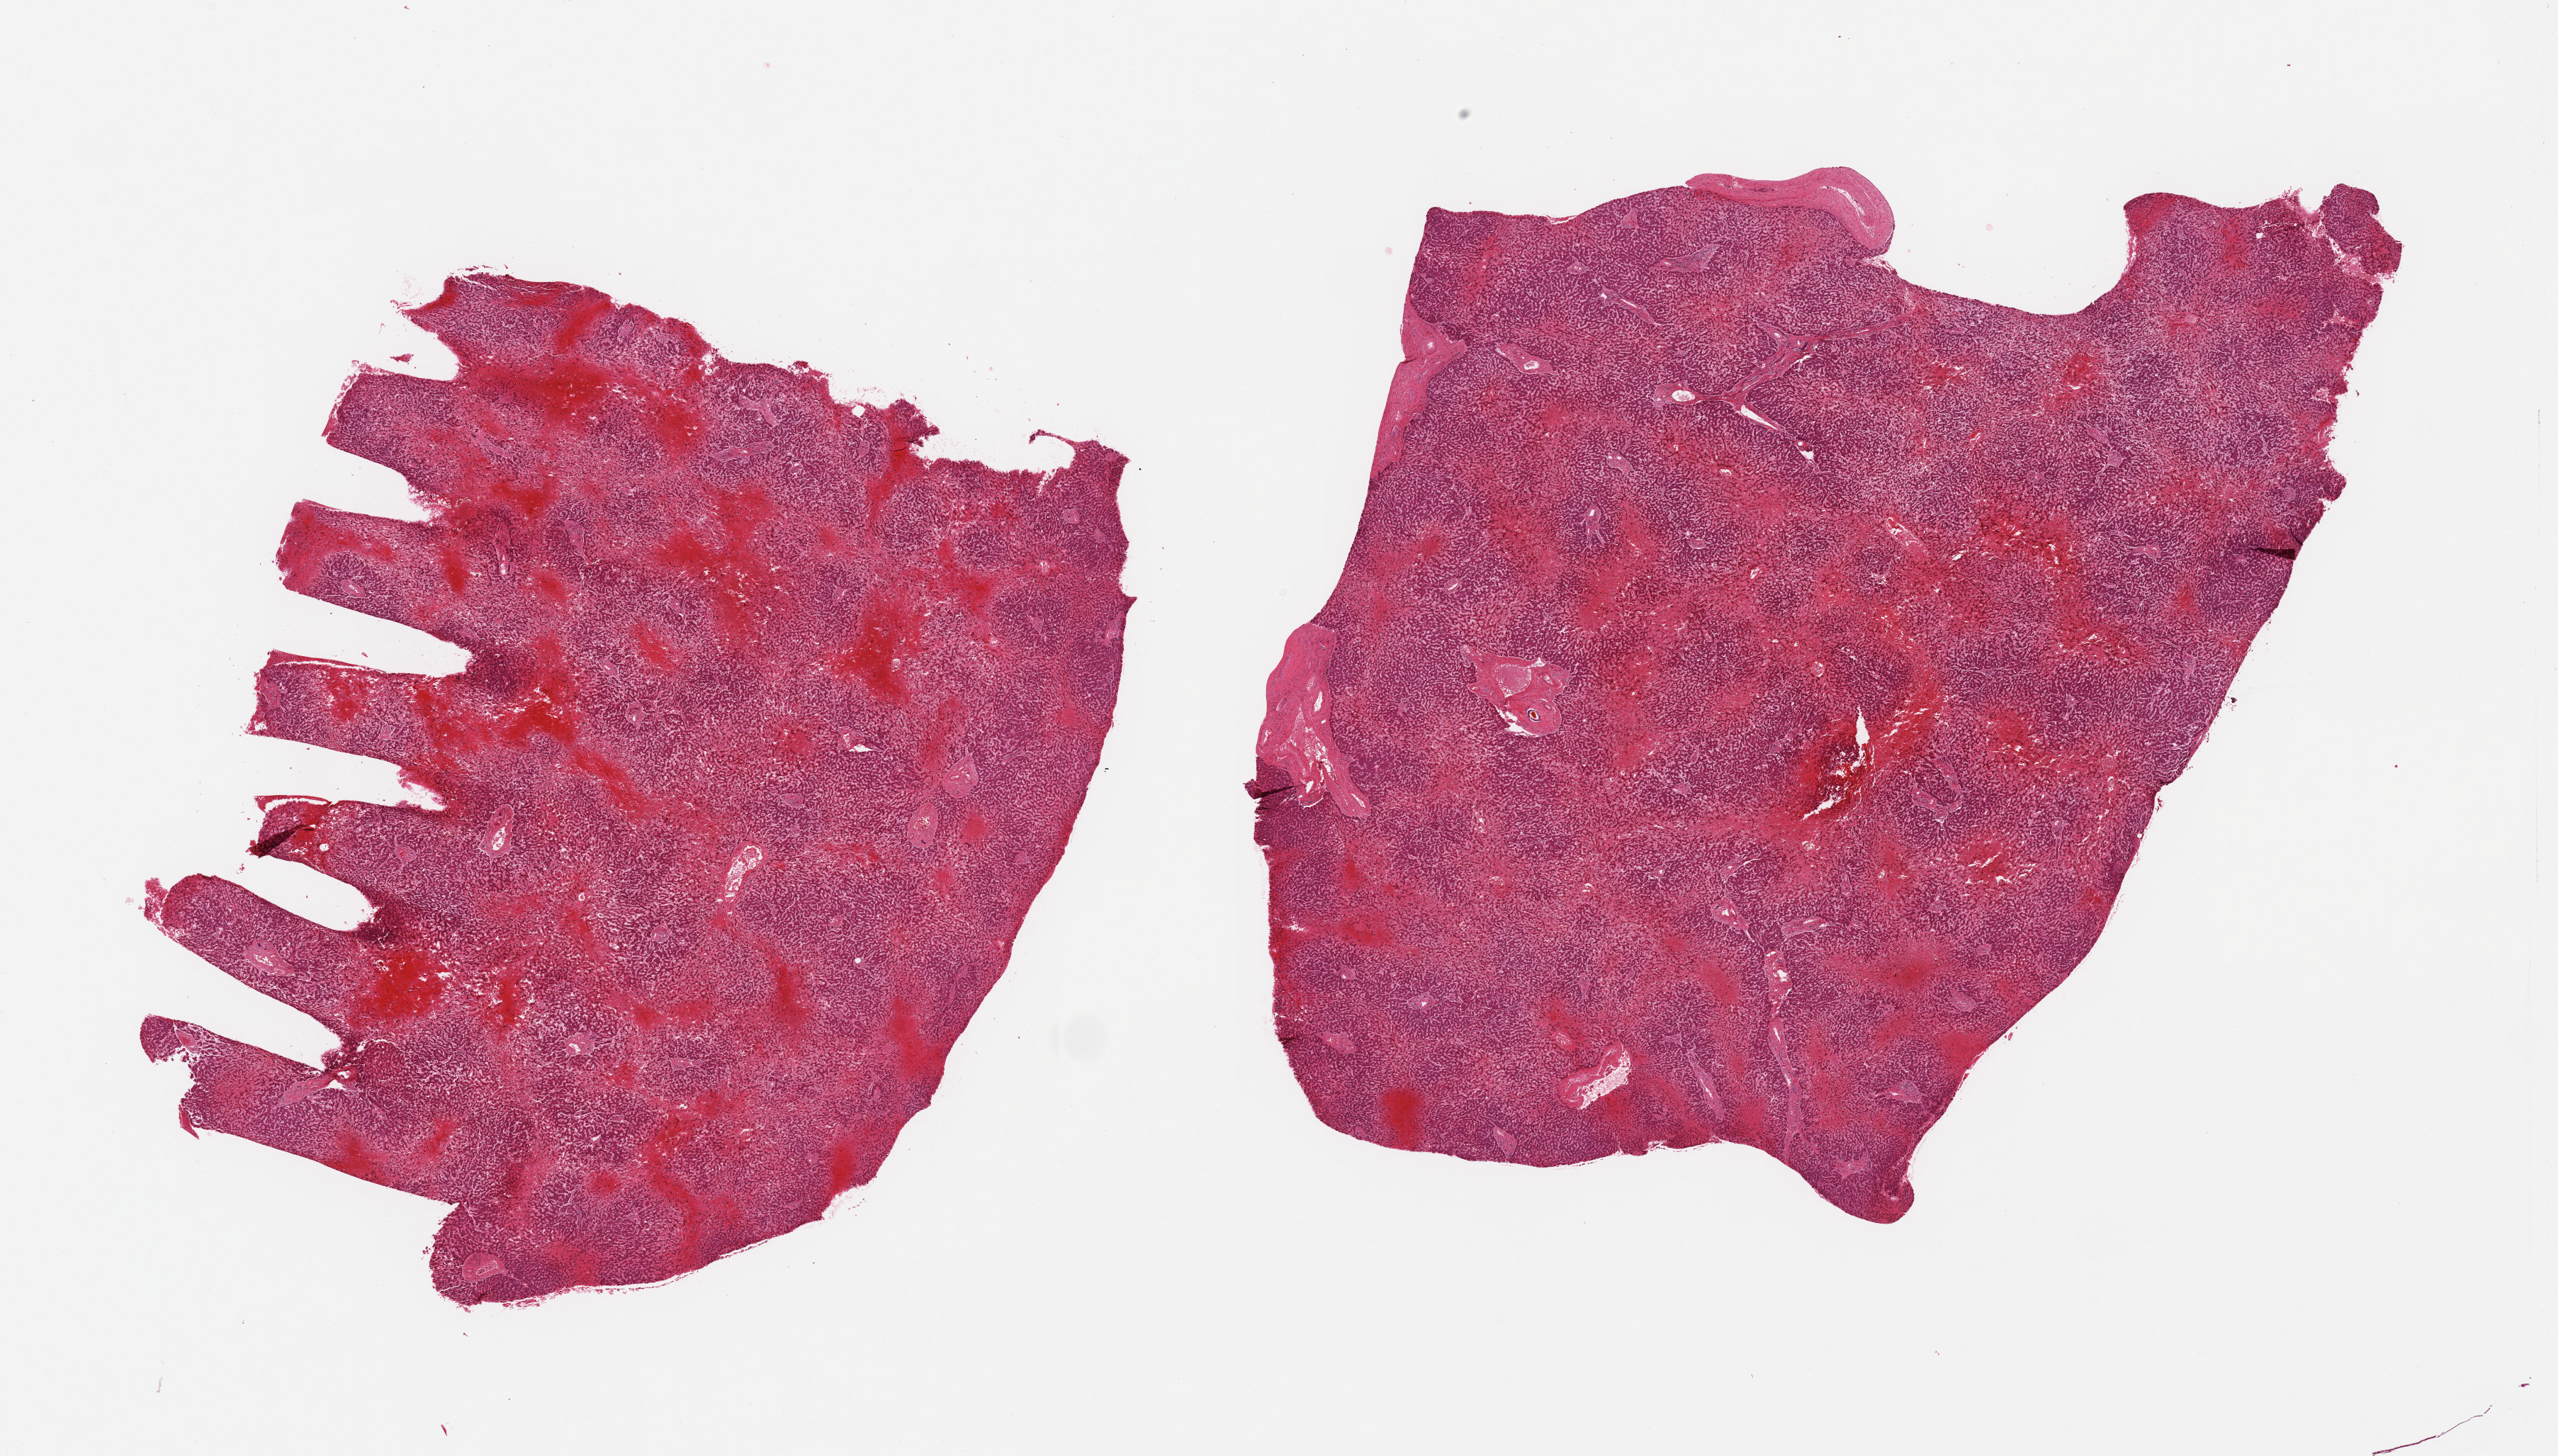
Haematoxylin and eosin whole-slide image — low-resolution overview of the scanned area, about 28.5 x 16.3 mm. PAXgene-fixed paraffin-embedded (PFPE) section. Section of liver (target tissue). Donor tissue sample. Male donor.
Pathologist's review note for this sample: 2 pieces; severe central congestion and cord cell atrophy.